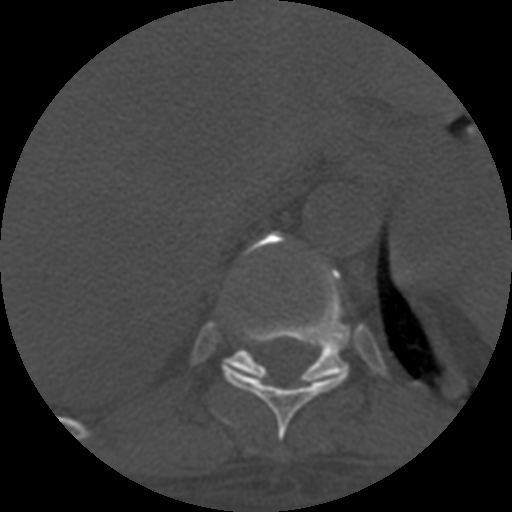
CT including the spine, one axial slice; position 348 of 708 along the scan axis; 120 kVp; one of 3 acquisitions stored at this slice position; bone window (W 1800 / L 400 HU); 512 × 512 image matrix, field of view 160 × 160 mm. Patient age 55 years. Case-level facts recorded for this patient, not image findings: primary cancer: colon; vertebrae with lytic lesions (as recorded): T12, L1, L5.
Structures marked on this image (semi-automatic segmentation, software-assisted and operator-edited):
- T10 vertebra: box from (x=223, y=368) to (x=347, y=440) px
- T11 vertebra: (x=223, y=234)–(x=350, y=386)